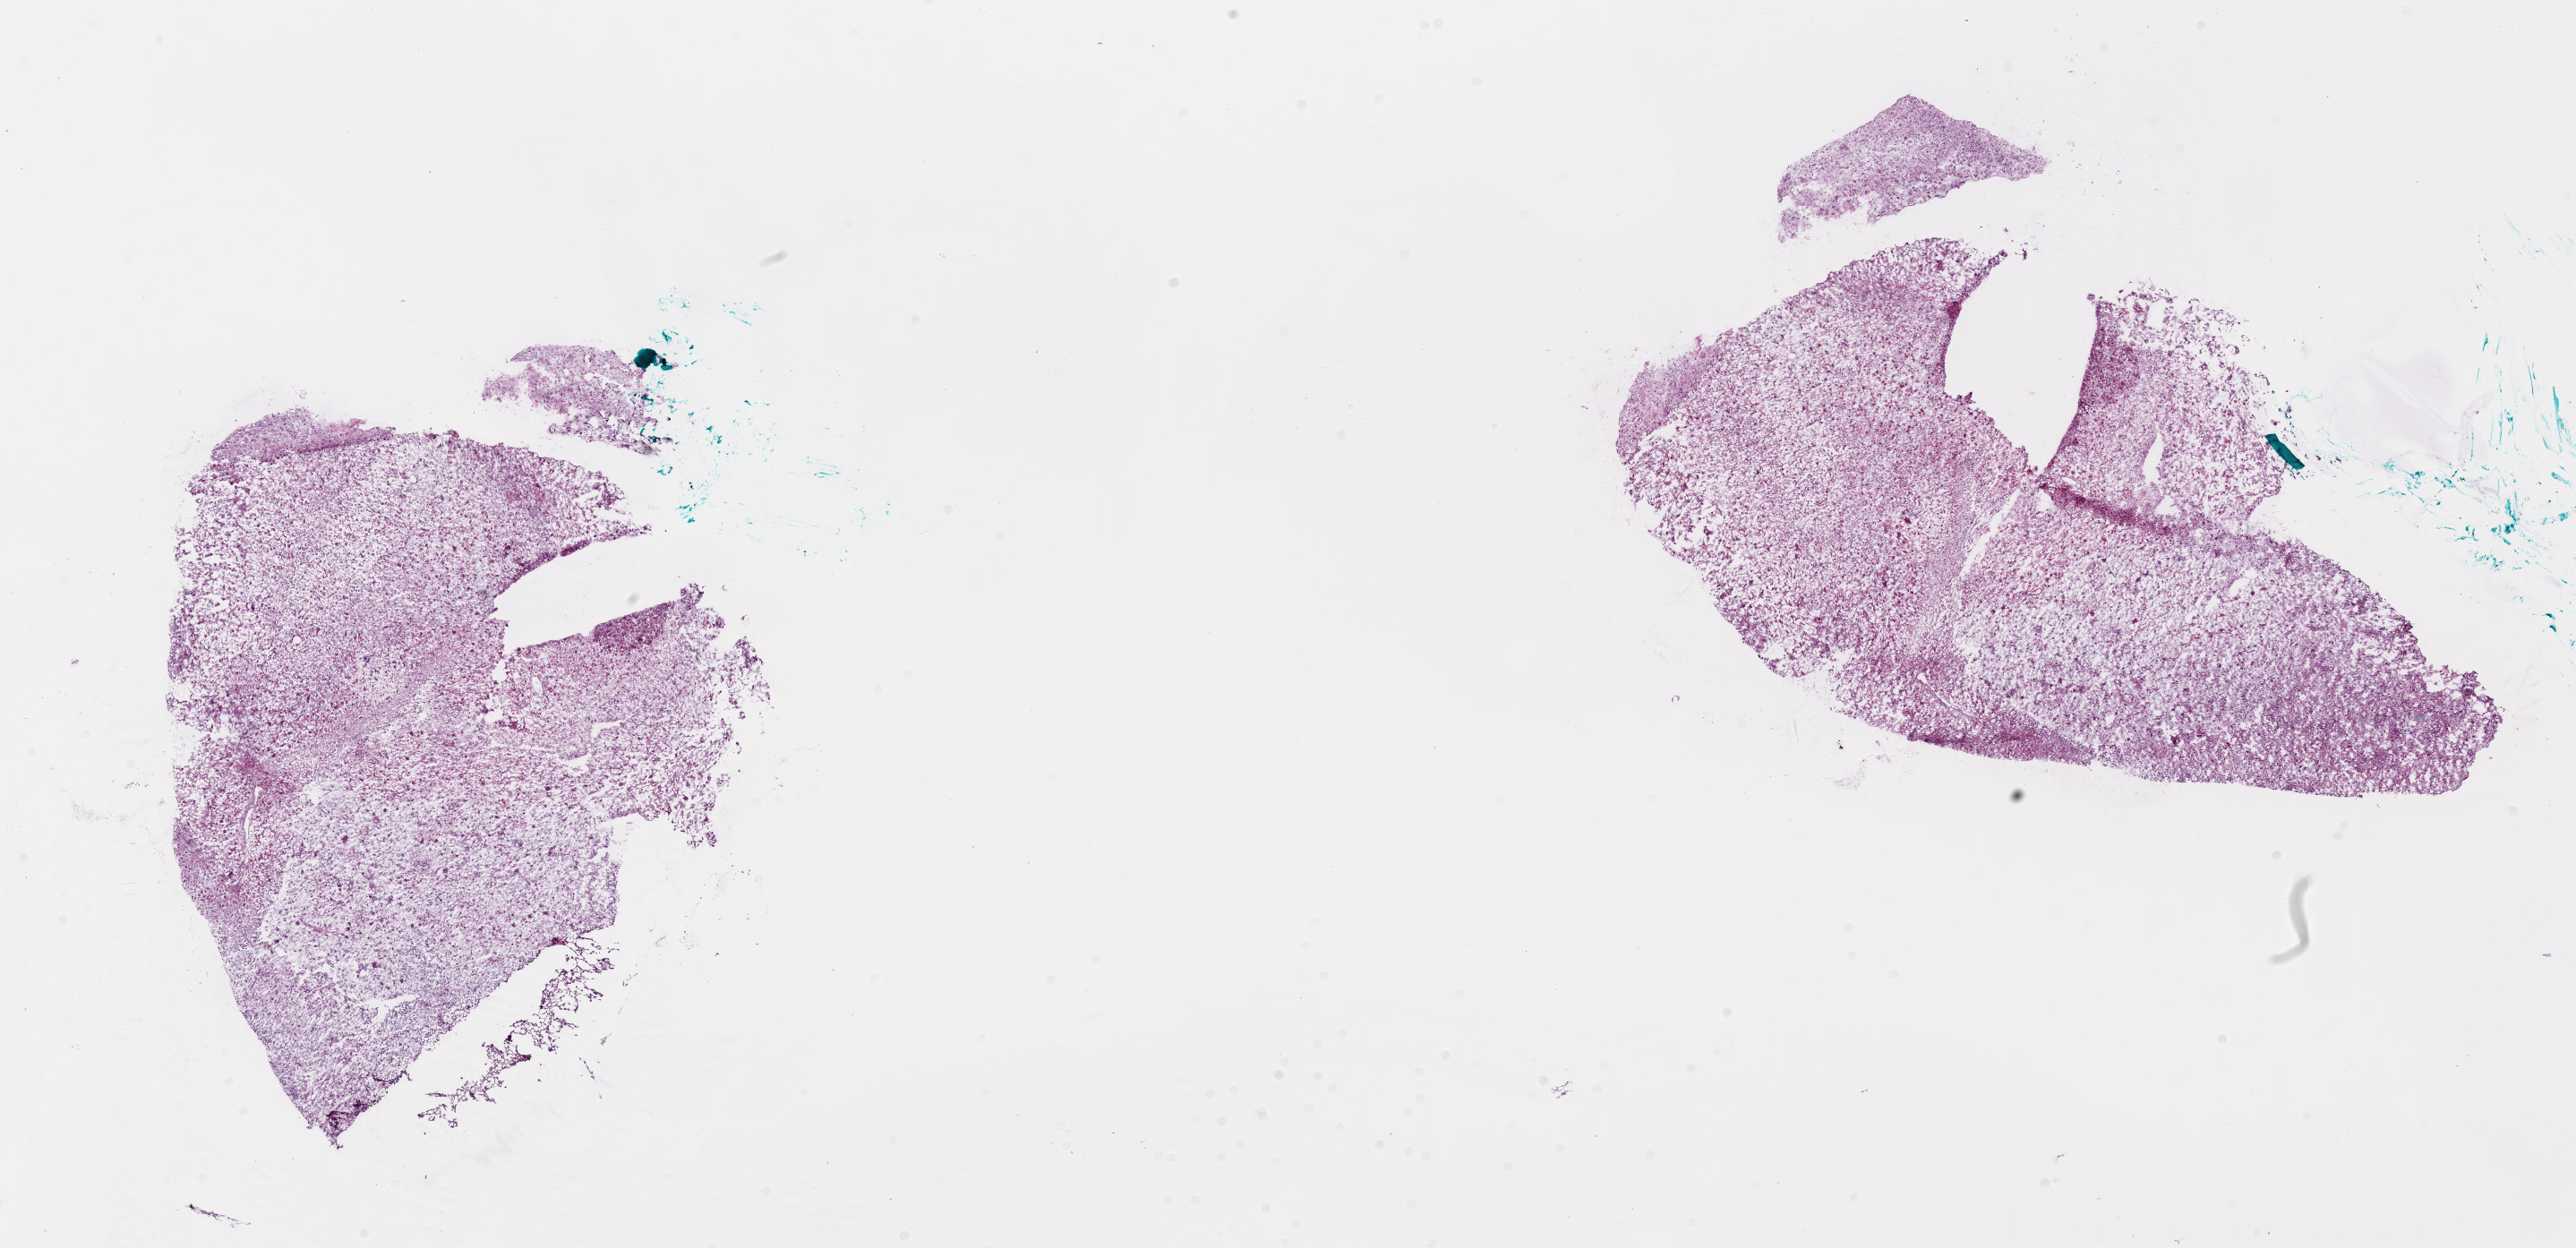
H&E-stained whole-slide image — a low-resolution overview of the entire scanned area, about 23.2 x 11.2 mm, frozen section from the bottom of the tissue portion, brain, primary tumour sample. Male, age 57 years at initial diagnosis. Composition of this section per pathologist review: tumour cells 85%, tumour nuclei 85%, normal cells 5%, stromal cells 10%, necrosis 0%.
- diagnosis: Glioblastoma